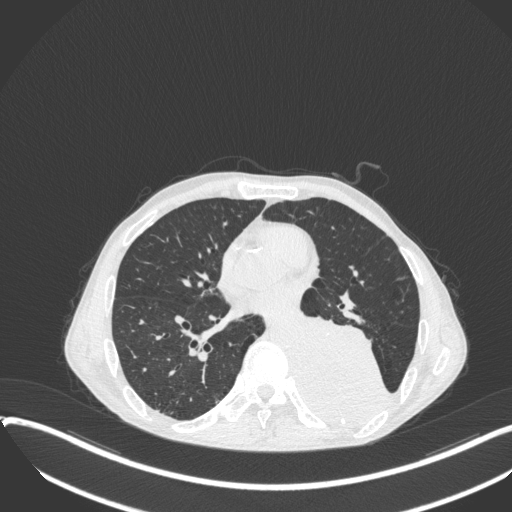
Chest CT, one axial slice; position 164 of 400 along the scan axis; lung window (W 1500 / L -600 HU); 1 mm slice thickness; 512 × 512 image matrix. Patient: male, 57 years. Case-level facts recorded for this patient, not image findings: clinical TNM (as recorded): T4 N0 M0.
Structures marked on this image (rectangle marked by the reading radiologist):
- lung tumour (recorded histology: squamous cell carcinoma): bounding box [x1, y1, x2, y2] px = [297, 307, 398, 436]